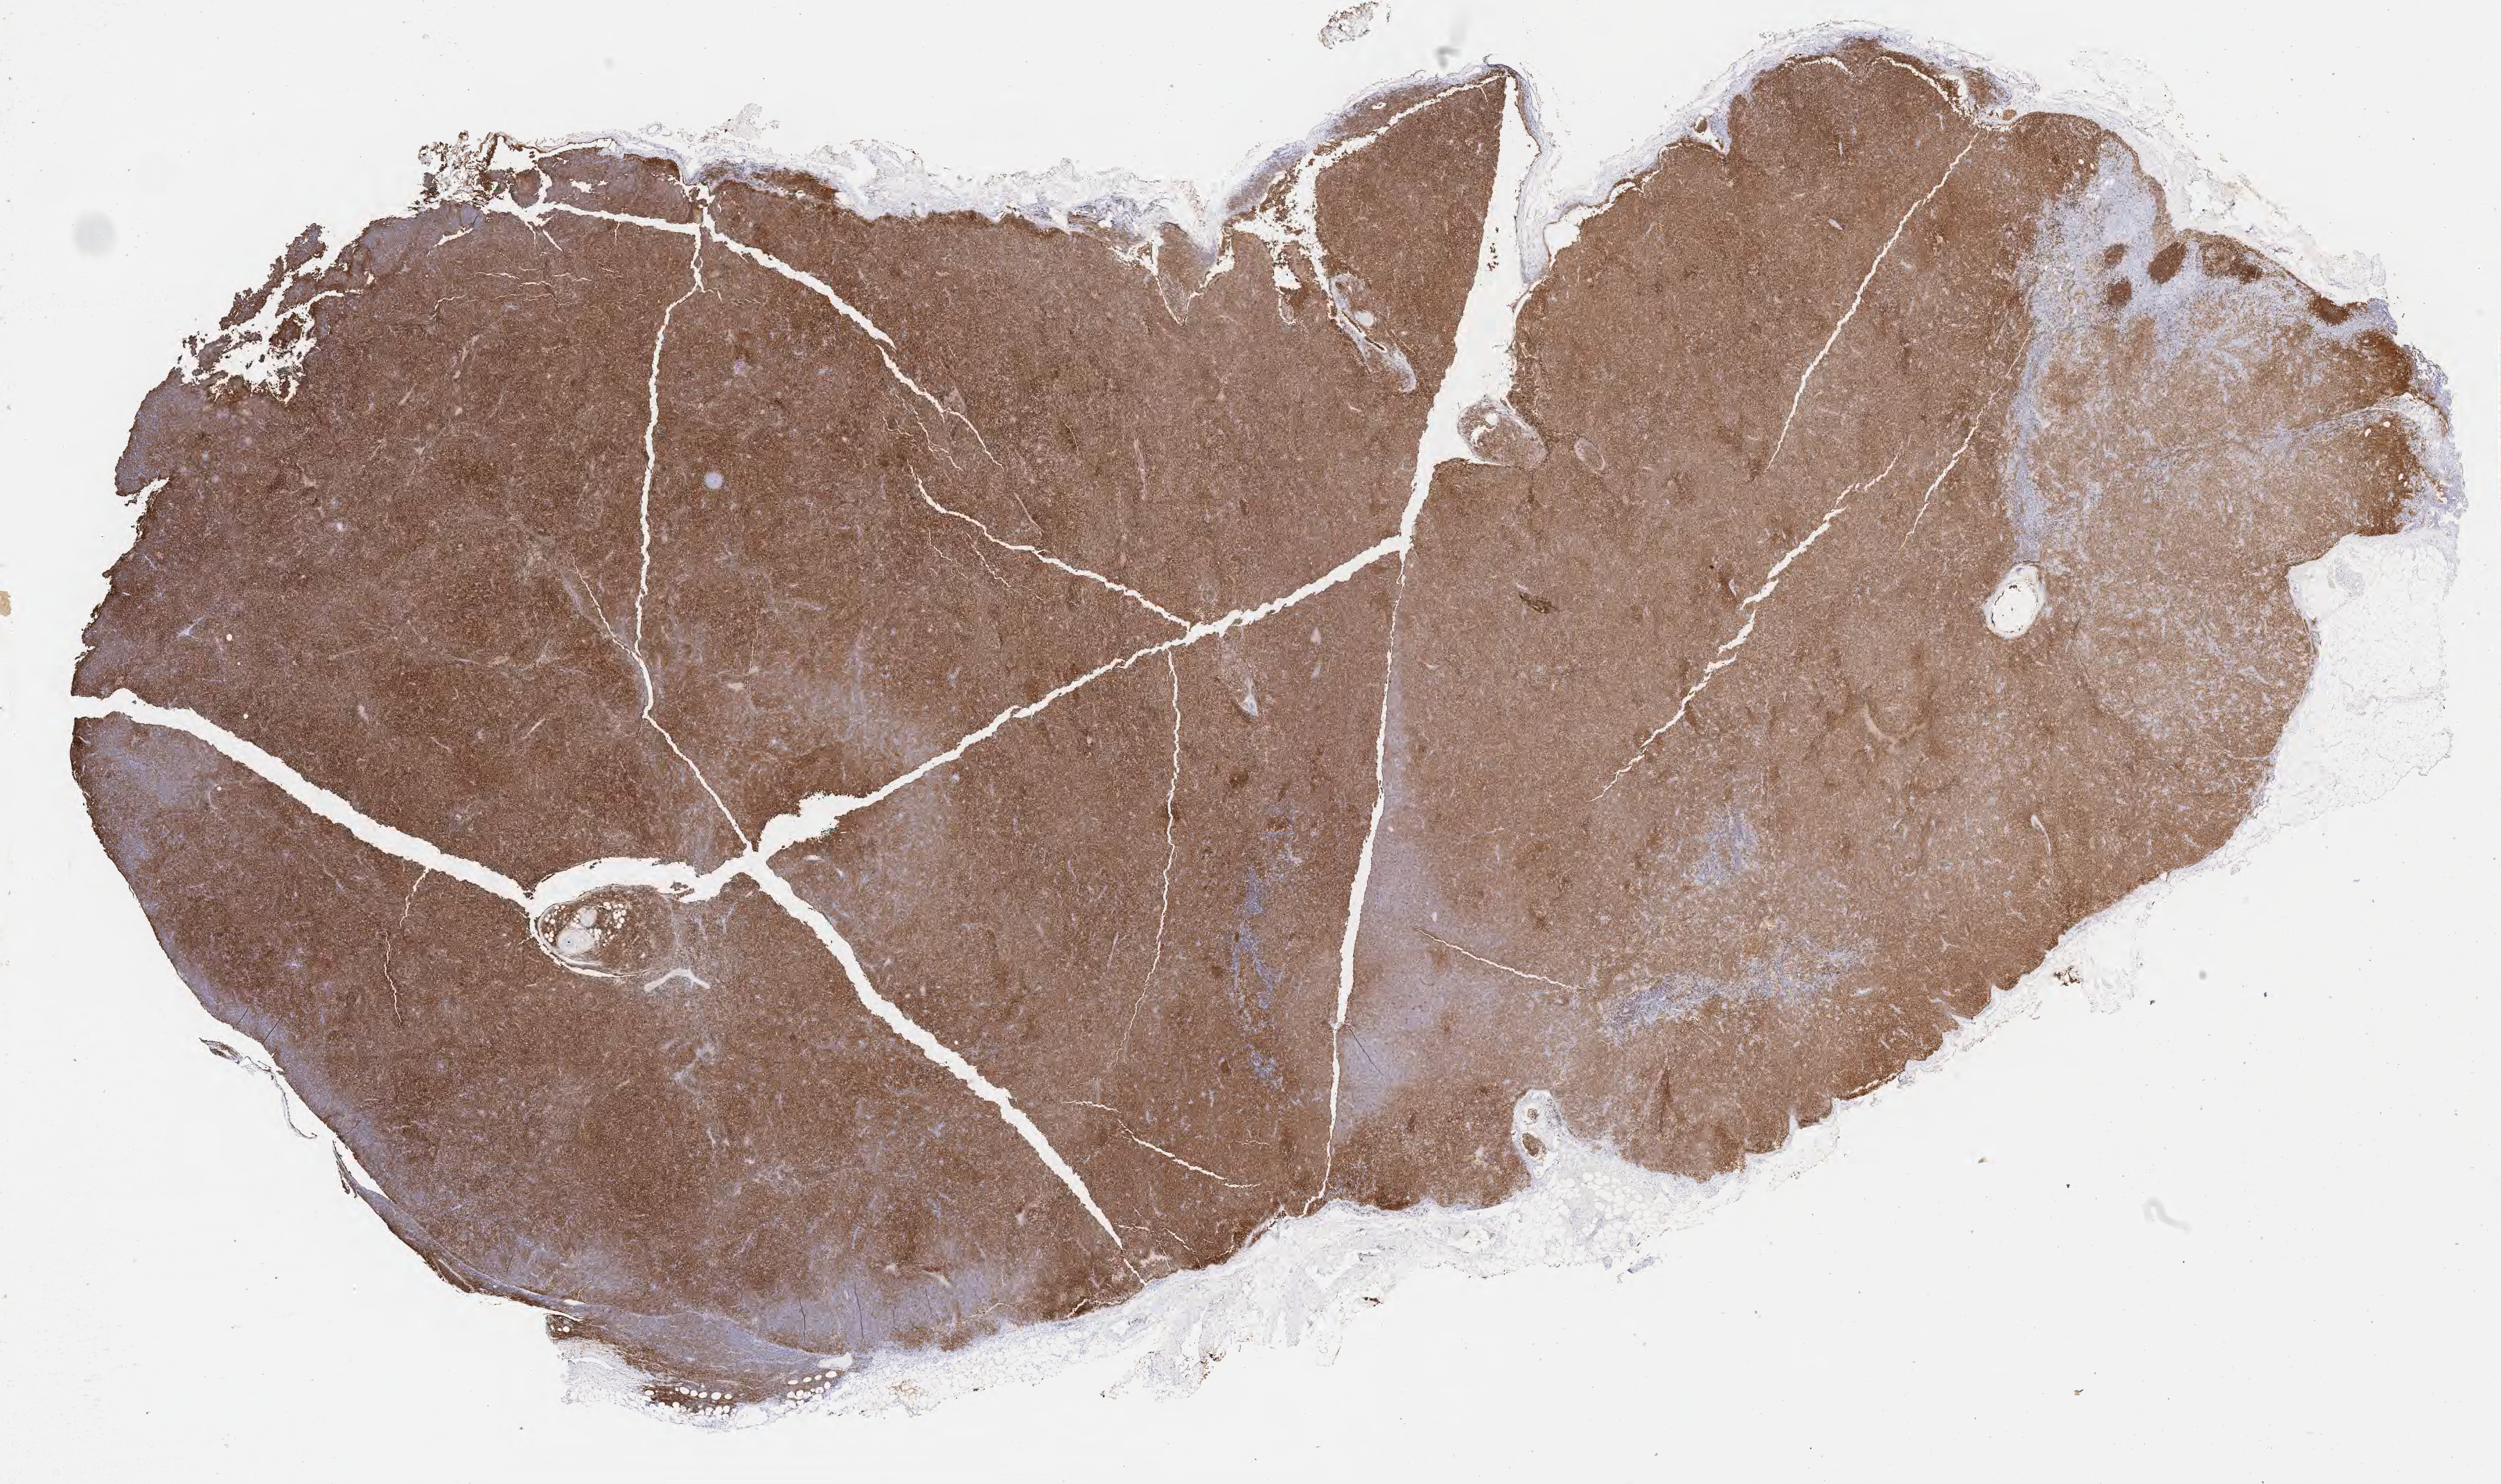
Whole-slide image, immunohistochemical stain for CD20 — low-resolution overview of the scanned area, about 29.2 x 17.3 mm; specimen: tumor tissue. Male patient, 69 years old.
Diagnosis: Diffuse large B-cell lymphoma, NOS.